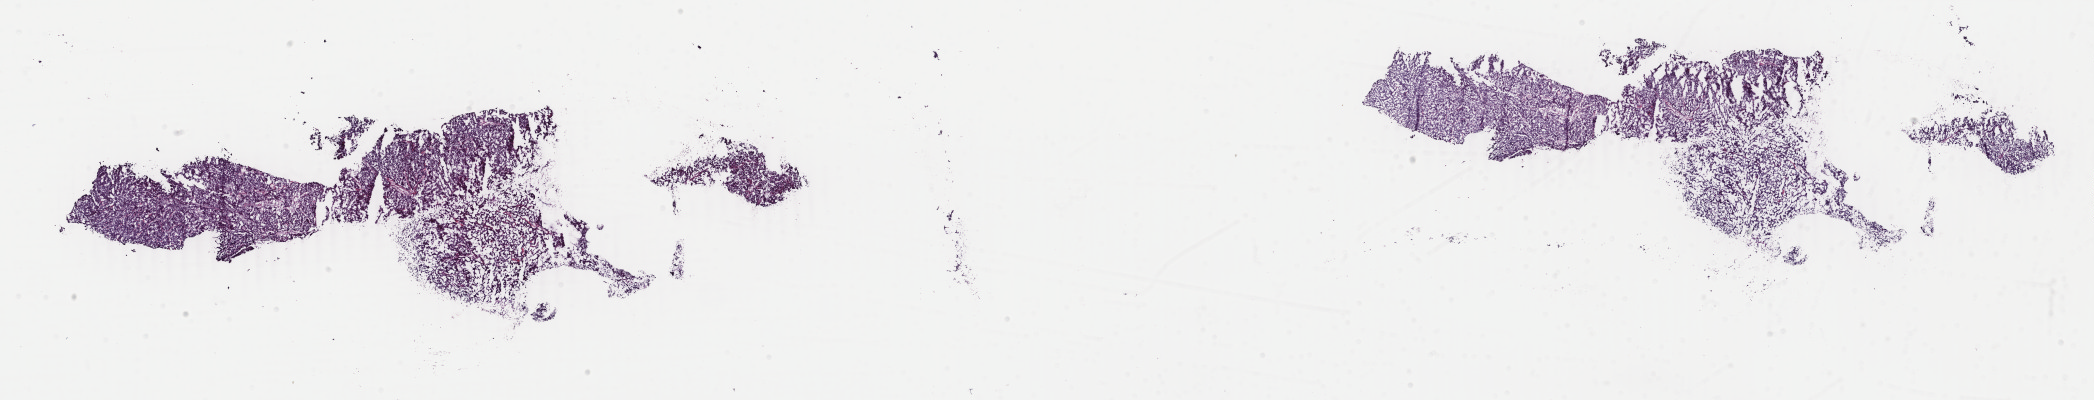
H&E whole-slide image, low-resolution overview of the scanned area, about 33.3 x 6.4 mm; frozen section; uterus, primary tumour sample. Patient sex: female. Histologic grade: G2 (moderately differentiated). Pathologist review of this section (percent, as recorded): tumour cells 70%, tumour nuclei 70%, normal cells 0%, stromal cells 25%, necrosis 5%. Inflammatory infiltration, as recorded: lymphocyte infiltration 40%, monocyte infiltration 20%, neutrophil infiltration 30%.
* FIGO stage: II
* histologic diagnosis: Endometrioid adenocarcinoma, NOS (endometrium)